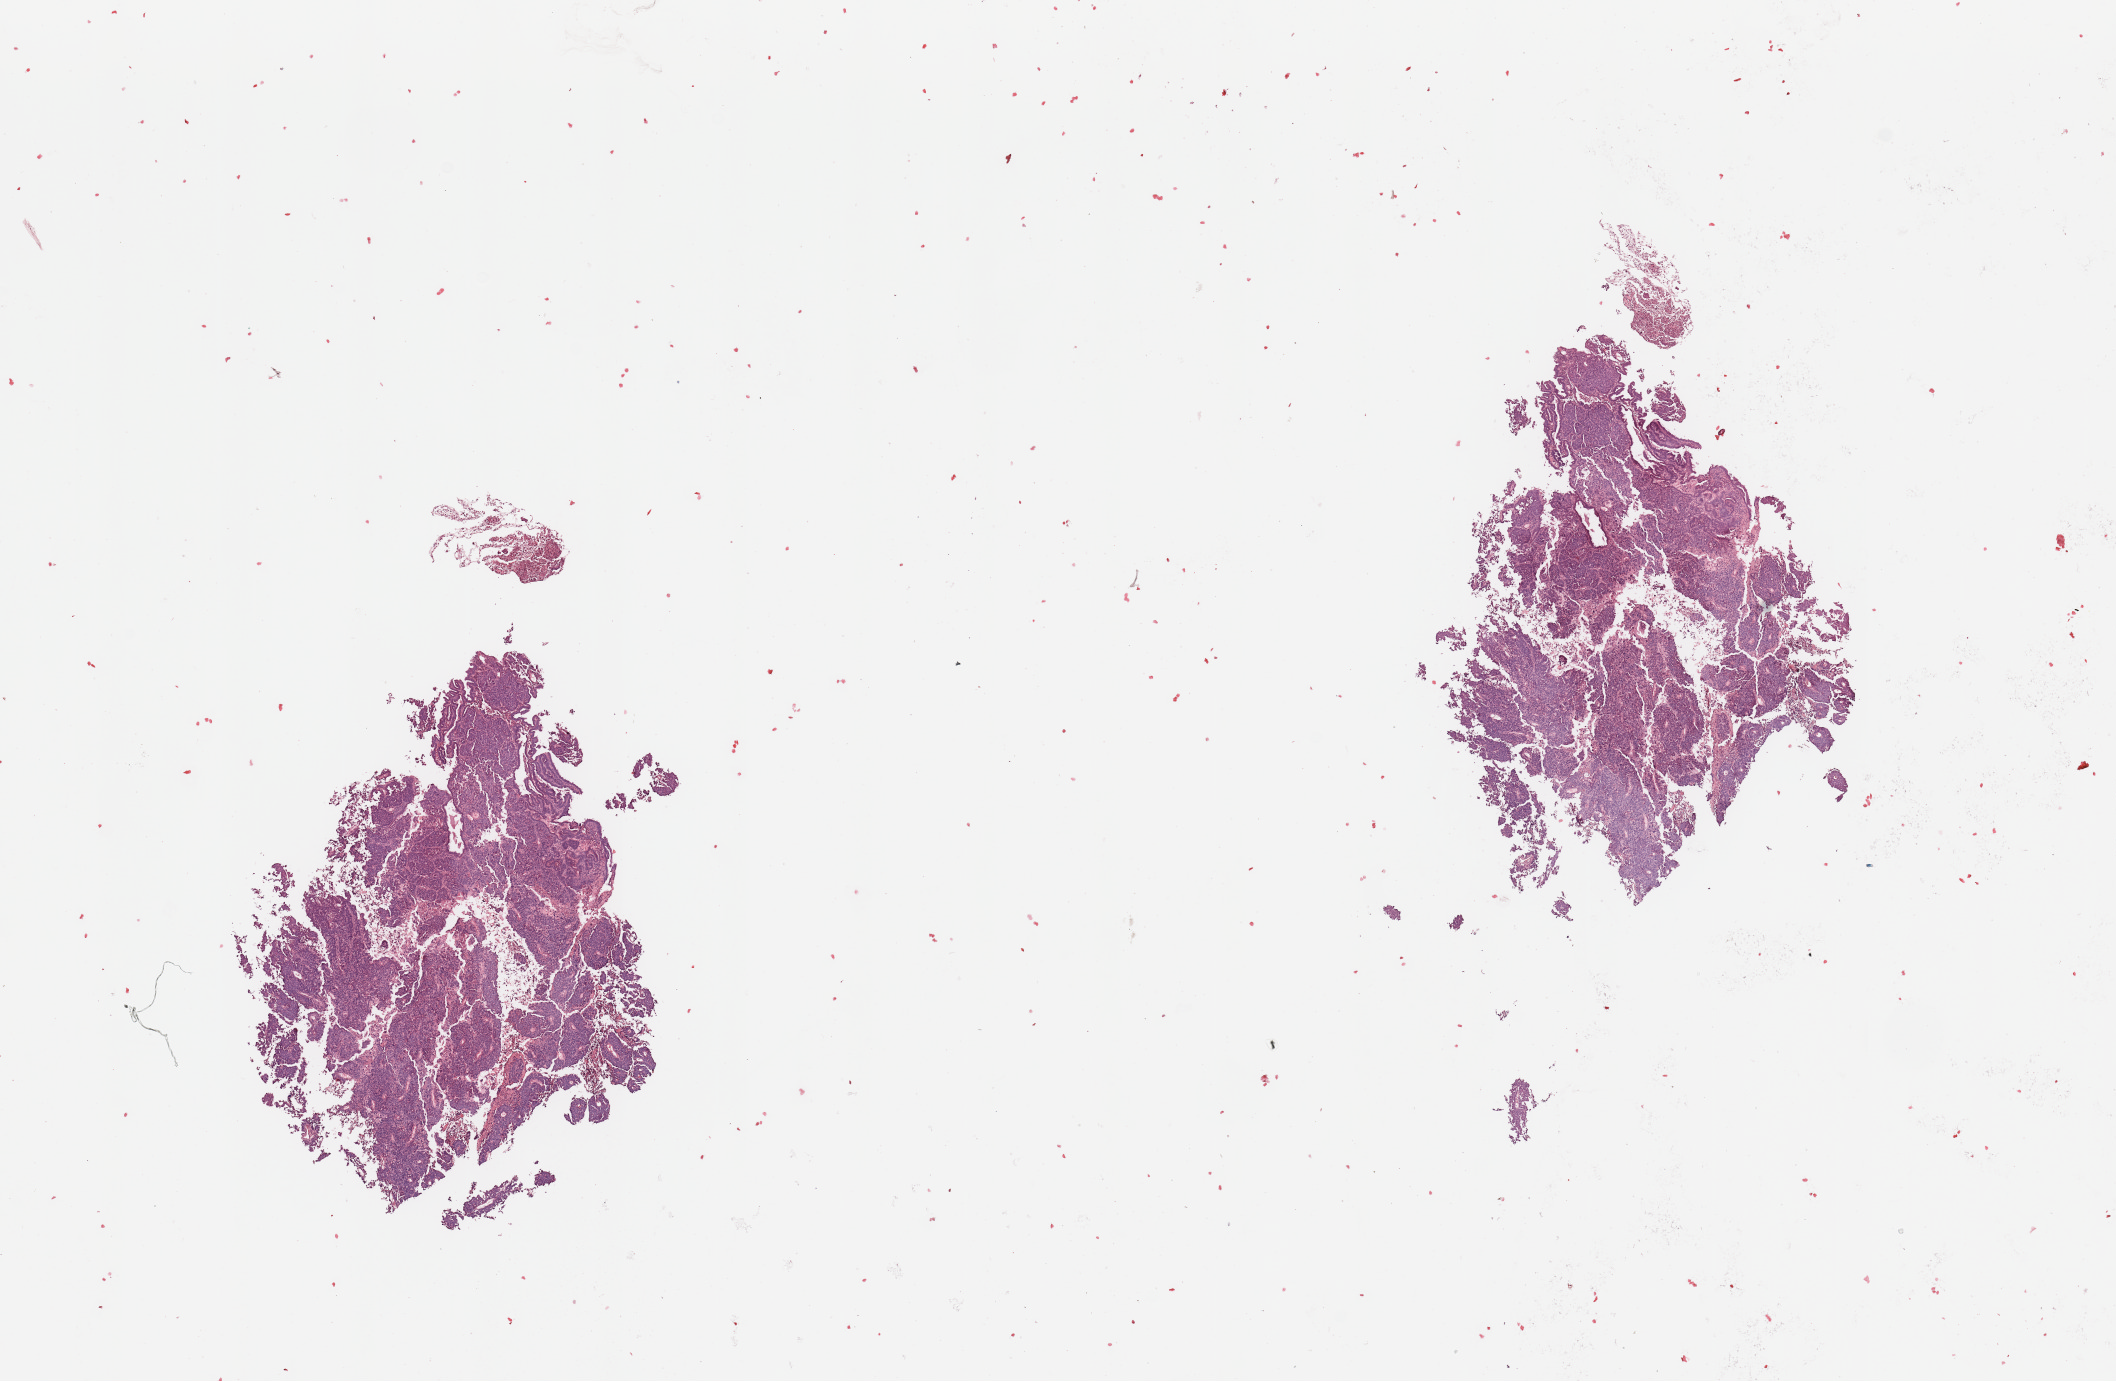
H&E-stained whole-slide image — a low-resolution overview of the entire scanned area, about 16.7 x 10.9 mm. Tumour tissue sample, sampled site: uterus. Patient: female, age 77 years. Histologic grade: G3 (poorly differentiated). Slide review estimates, as recorded: tumour nuclei 85%, necrosis 5%.
AJCC pathologic stage: I. Histologic diagnosis: Endometrioid adenocarcinoma, NOS. Primary tumour site (as recorded): anterior endometrium.